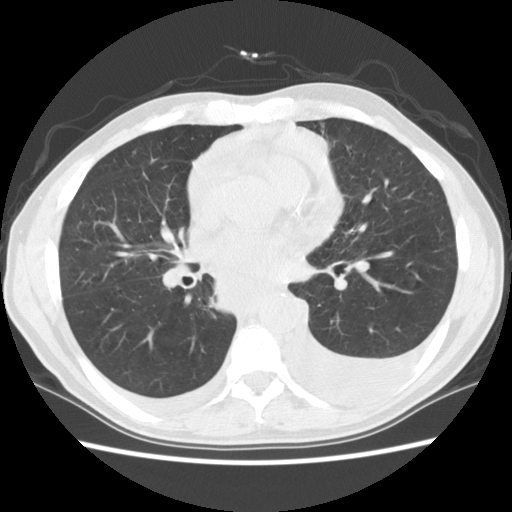
Low-dose screening chest CT, axial slice, first (baseline) screen, lung window (W 1500 / L -600 HU), standard (soft-tissue) reconstruction kernel (STANDARD), 140 kVp. Male, age 60 years at enrolment.
Expert reader's lesion annotation, bounding box <174,241,307,333> (left, top, right, bottom; pixels). Screening reader's record for this exam: no non-calcified nodule ≥4 mm recorded. Later outcome: lung cancer diagnosed 12 days after this screen — squamous cell carcinoma, NOS, carina, poorly differentiated (G3), stage IV (AJCC 6th edition).